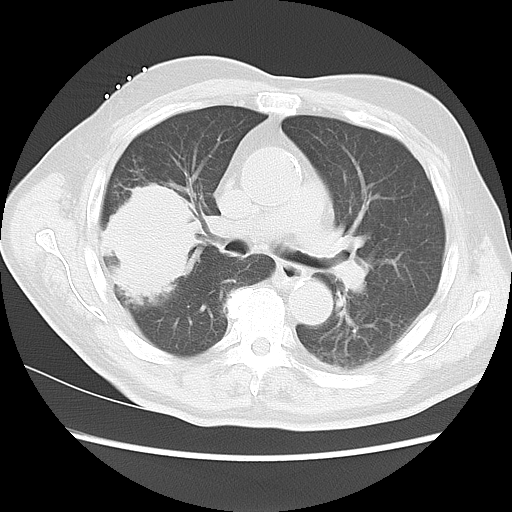
Chest CT, one axial slice. Position 7 of 15 along the scan axis. Reconstruction kernel LUNG. 120 kVp. Lung window (W 1500 / L -600 HU). 5 mm slice thickness. 512 × 512 image matrix. Patient: male, 68 years. From the clinical record (not read from this slice): clinical TNM (as recorded): T4 N3 M0.
Outlined on this slice (rectangle marked by the reading radiologist):
- lung tumour (recorded histology: squamous cell carcinoma): box from (x=104, y=176) to (x=201, y=305) px